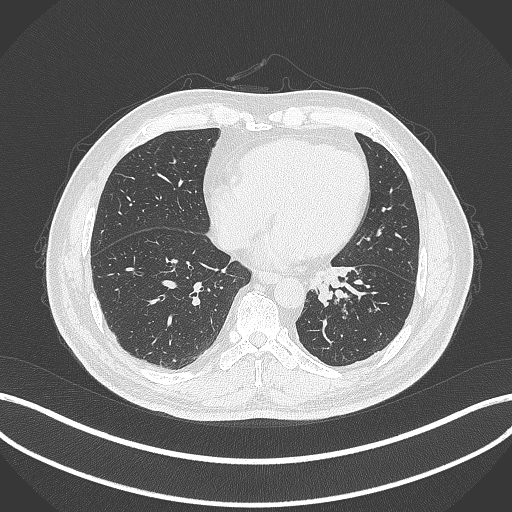
Chest CT, one axial slice; position 89 of 312 along the scan axis; reconstruction kernel B70f; lung window (W 1500 / L -600 HU); 1 mm slice thickness; 512 × 512 image matrix, field of view 400 × 400 mm. Male patient, age 71 years. From the clinical record (not read from this slice): clinical TNM (as recorded): T1b N0 M0.
Structures marked on this image (bounding box drawn by a radiologist):
- lung tumour (recorded histology: squamous cell carcinoma): bounding box (x1, y1, x2, y2) in pixels: (307, 265, 361, 307)